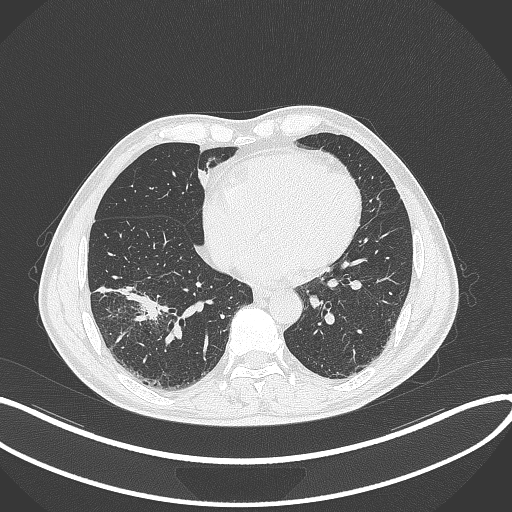
Chest CT, one axial slice; slice 128 of 364 in the series (ordered by position); lung window (W 1500 / L -600 HU); 1 mm slice thickness; 512 × 512 image matrix, field of view 400 × 400 mm. Patient: male, 58 years. From the clinical record (not read from this slice): clinical TNM (as recorded): T3 N0 M0.
Outlined on this slice (bounding box drawn by a radiologist):
- lung tumour (recorded histology: squamous cell carcinoma): bounding box (x1, y1, x2, y2) in pixels: (129, 294, 160, 322)